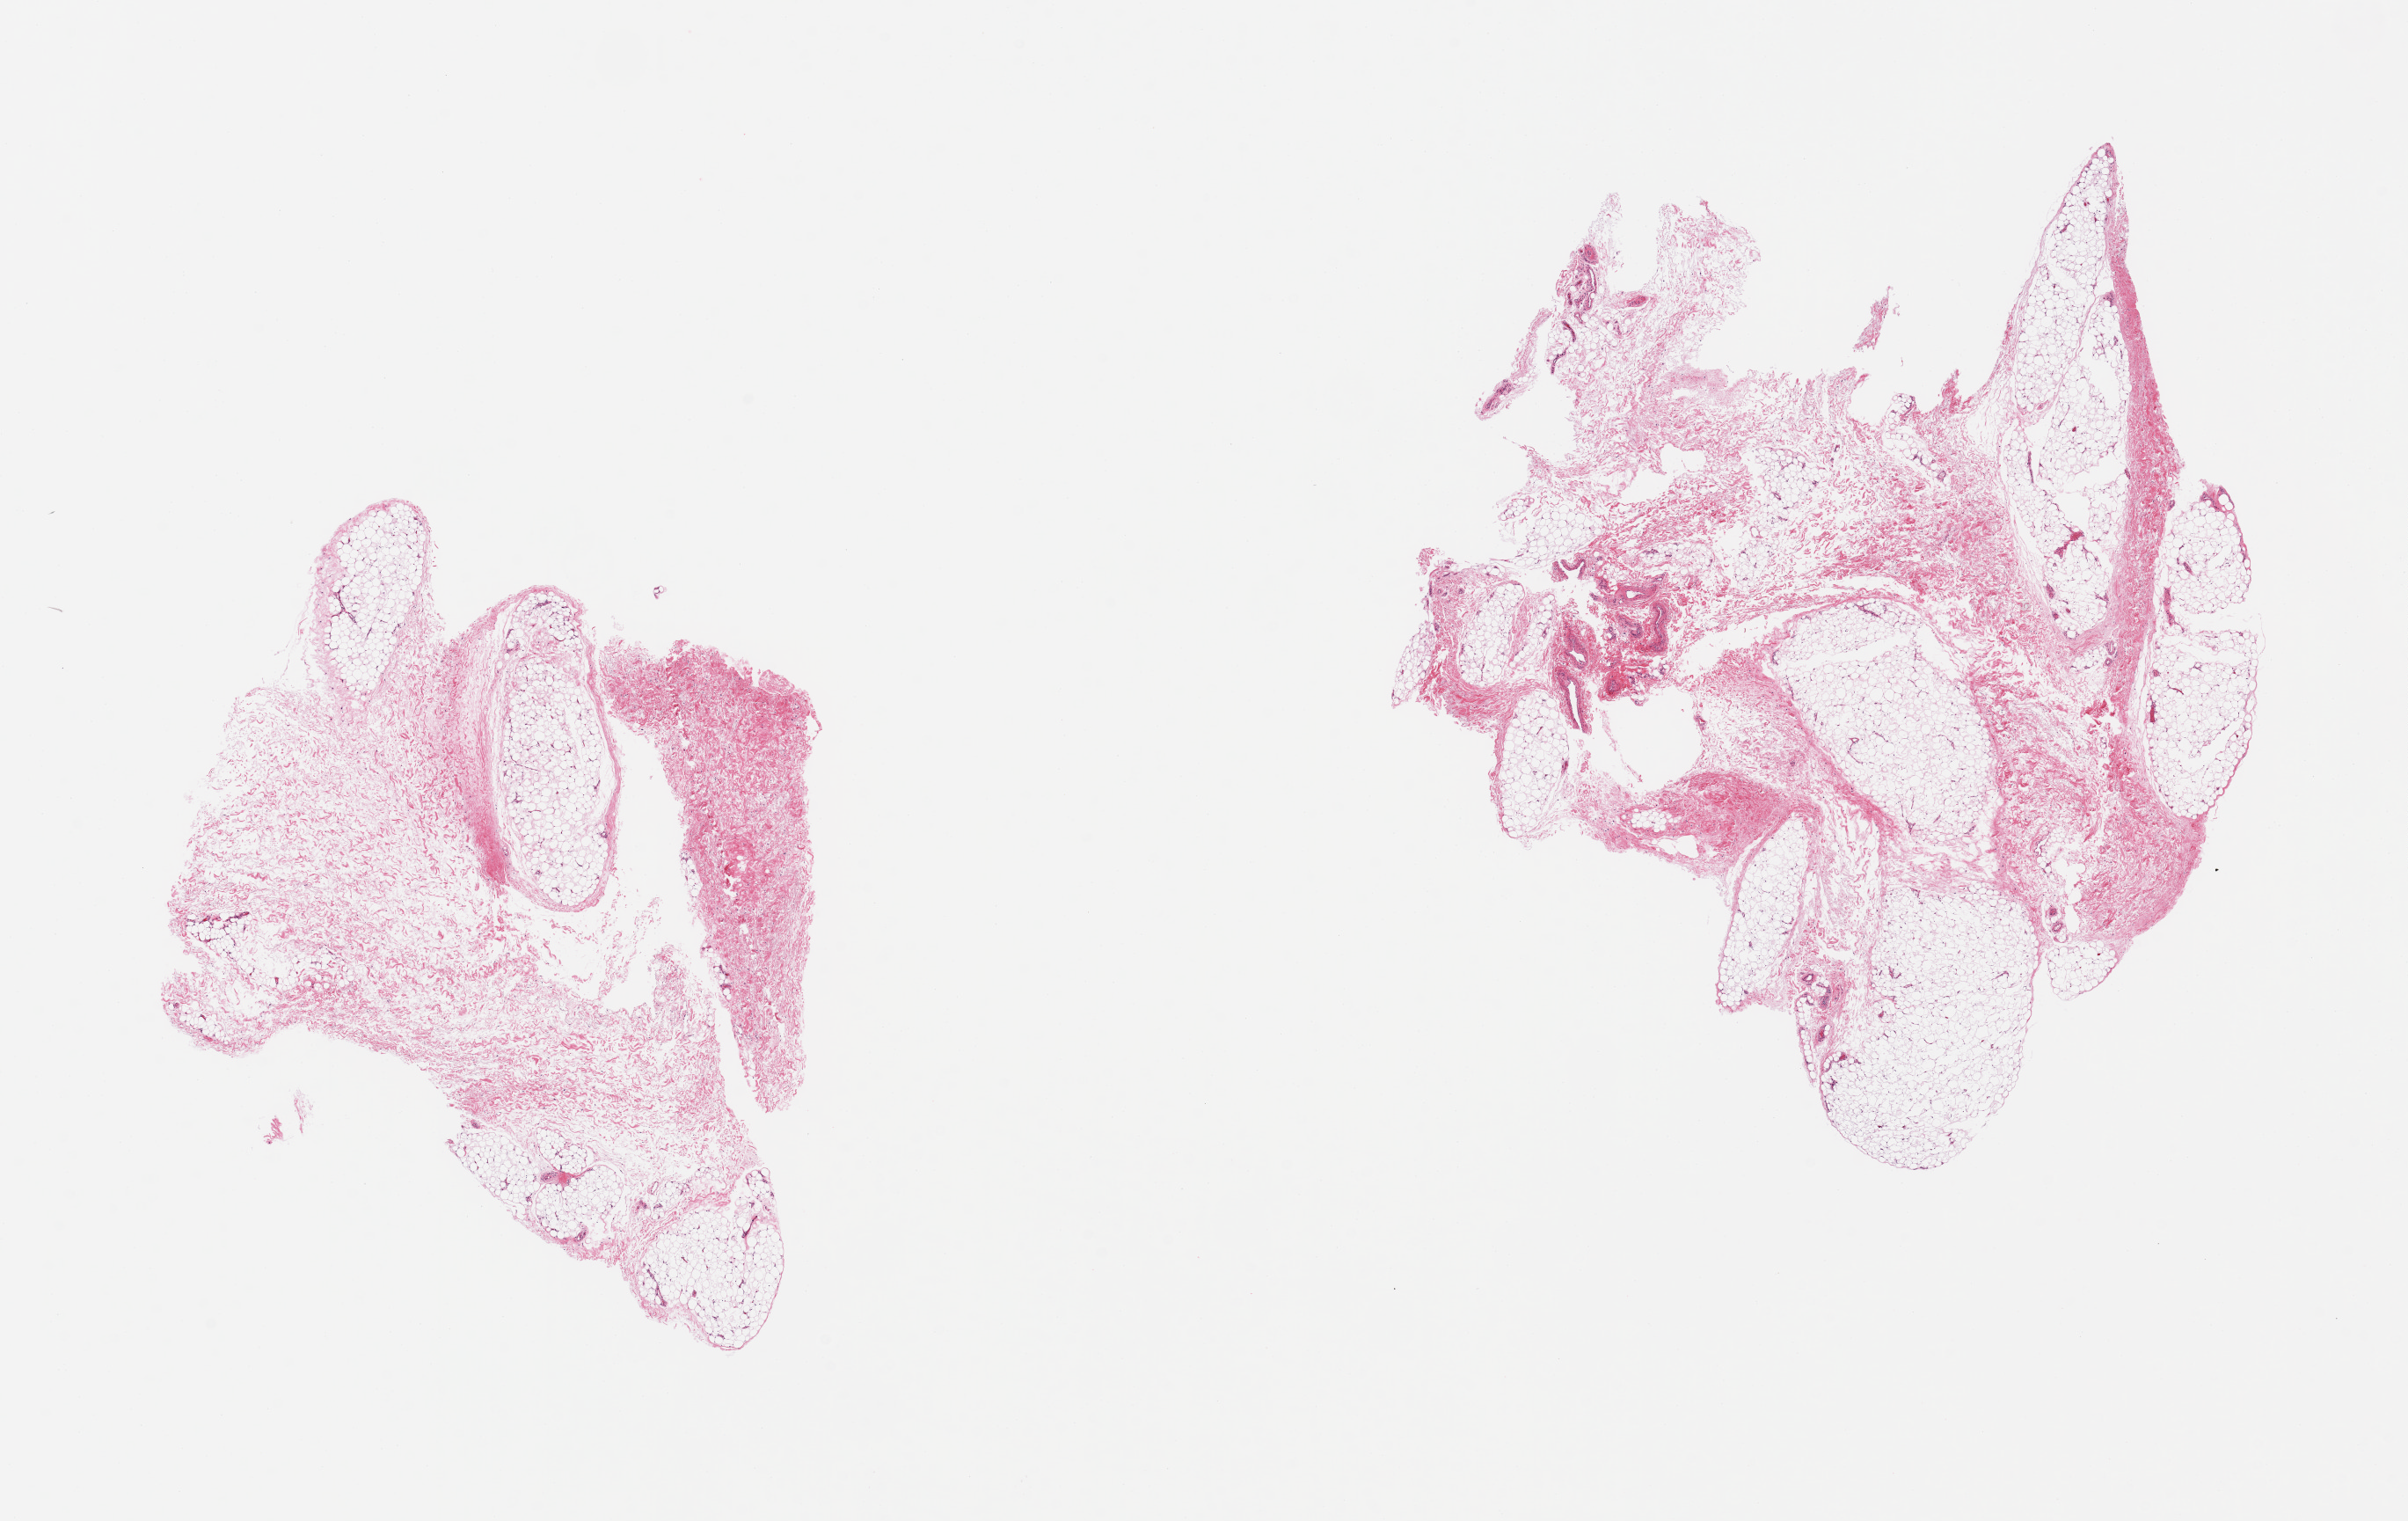
Haematoxylin and eosin whole-slide image, a low-resolution overview of the entire scanned area, about 21.7 x 13.7 mm. PAXgene-fixed, paraffin-embedded tissue. Sampled site (target tissue): adipose tissue. Donor tissue sample. Male donor.
• review note (as recorded): 2 pieces; 10% fibrovascular content